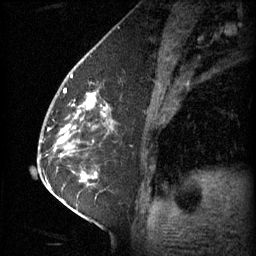
Breast MRI (dynamic contrast-enhanced), one sagittal slice; 3 images stored at this slice position (order not interpretable as contrast timing); 1.5 T; TE 4.2 ms, TR 11 ms; 2 mm slice thickness; 256 × 256 image matrix. Female patient, age 62 years.
Structures marked on this image (semi-automatic segmentation, software-assisted and operator-edited):
- analysis volume of interest (the breast-tissue region the enhancement analysis was run in; not a lesion): bounding box <55,72,115,135> (left, top, right, bottom; pixels)
- tumour enhancement mask (voxels above the 70 % enhancement threshold inside the analysis volume of interest): <63,94,106,133>